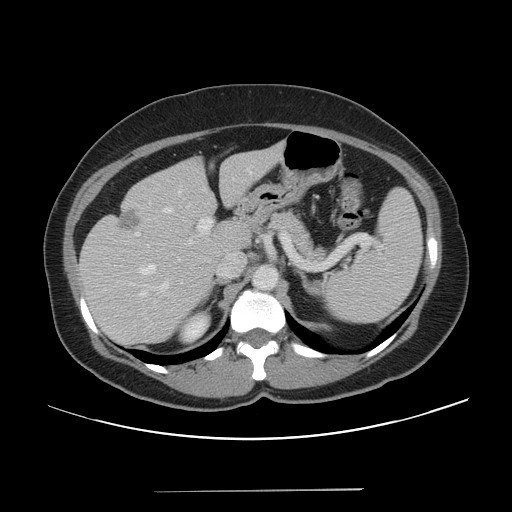
Contrast-enhanced abdominal CT, one axial slice. Slice 28 of 56 in the series (ordered by position). 120 kVp. Intravenous contrast given. Soft-tissue window (W 400 / L 40 HU). 5 mm slice thickness. 512 × 512 image matrix, field of view 419 × 419 mm. Female patient, age 54 years. Case-level facts recorded for this patient, not image findings: diagnosis: colorectal cancer liver metastases, imaged before liver resection; multiple liver metastases: yes; largest metastasis: 3.2 cm; disease in both lobes: yes.
Annotated regions visible in this slice (manually delineated by an expert):
- hepatic veins: bounding box (x1, y1, x2, y2) in pixels: (140, 192, 191, 296)
- liver: (80, 144, 285, 346)
- planned liver remnant (the part of the liver to remain after resection): (175, 143, 285, 250)
- portal vein (with intrahepatic branches): (160, 178, 301, 290)
- liver metastasis: (118, 209, 139, 231)